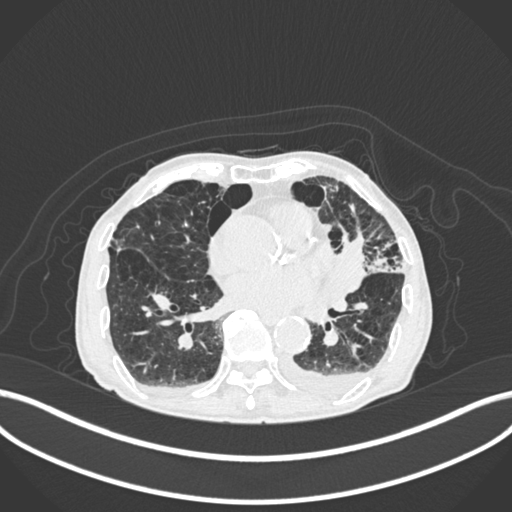
Chest CT, one axial slice. Reconstruction kernel B30f. 120 kVp. Lung window (W 1500 / L -600 HU). 512 × 512 image matrix, field of view 400 × 400 mm. Male patient, age 90 years or older. Case-level facts recorded for this patient, not image findings: clinical TNM (as recorded): T2b N1 M0.
Structures marked on this image (rectangle marked by the reading radiologist):
- lung tumour (recorded histology: squamous cell carcinoma): bounding box (x1, y1, x2, y2) in pixels: (336, 225, 370, 294)